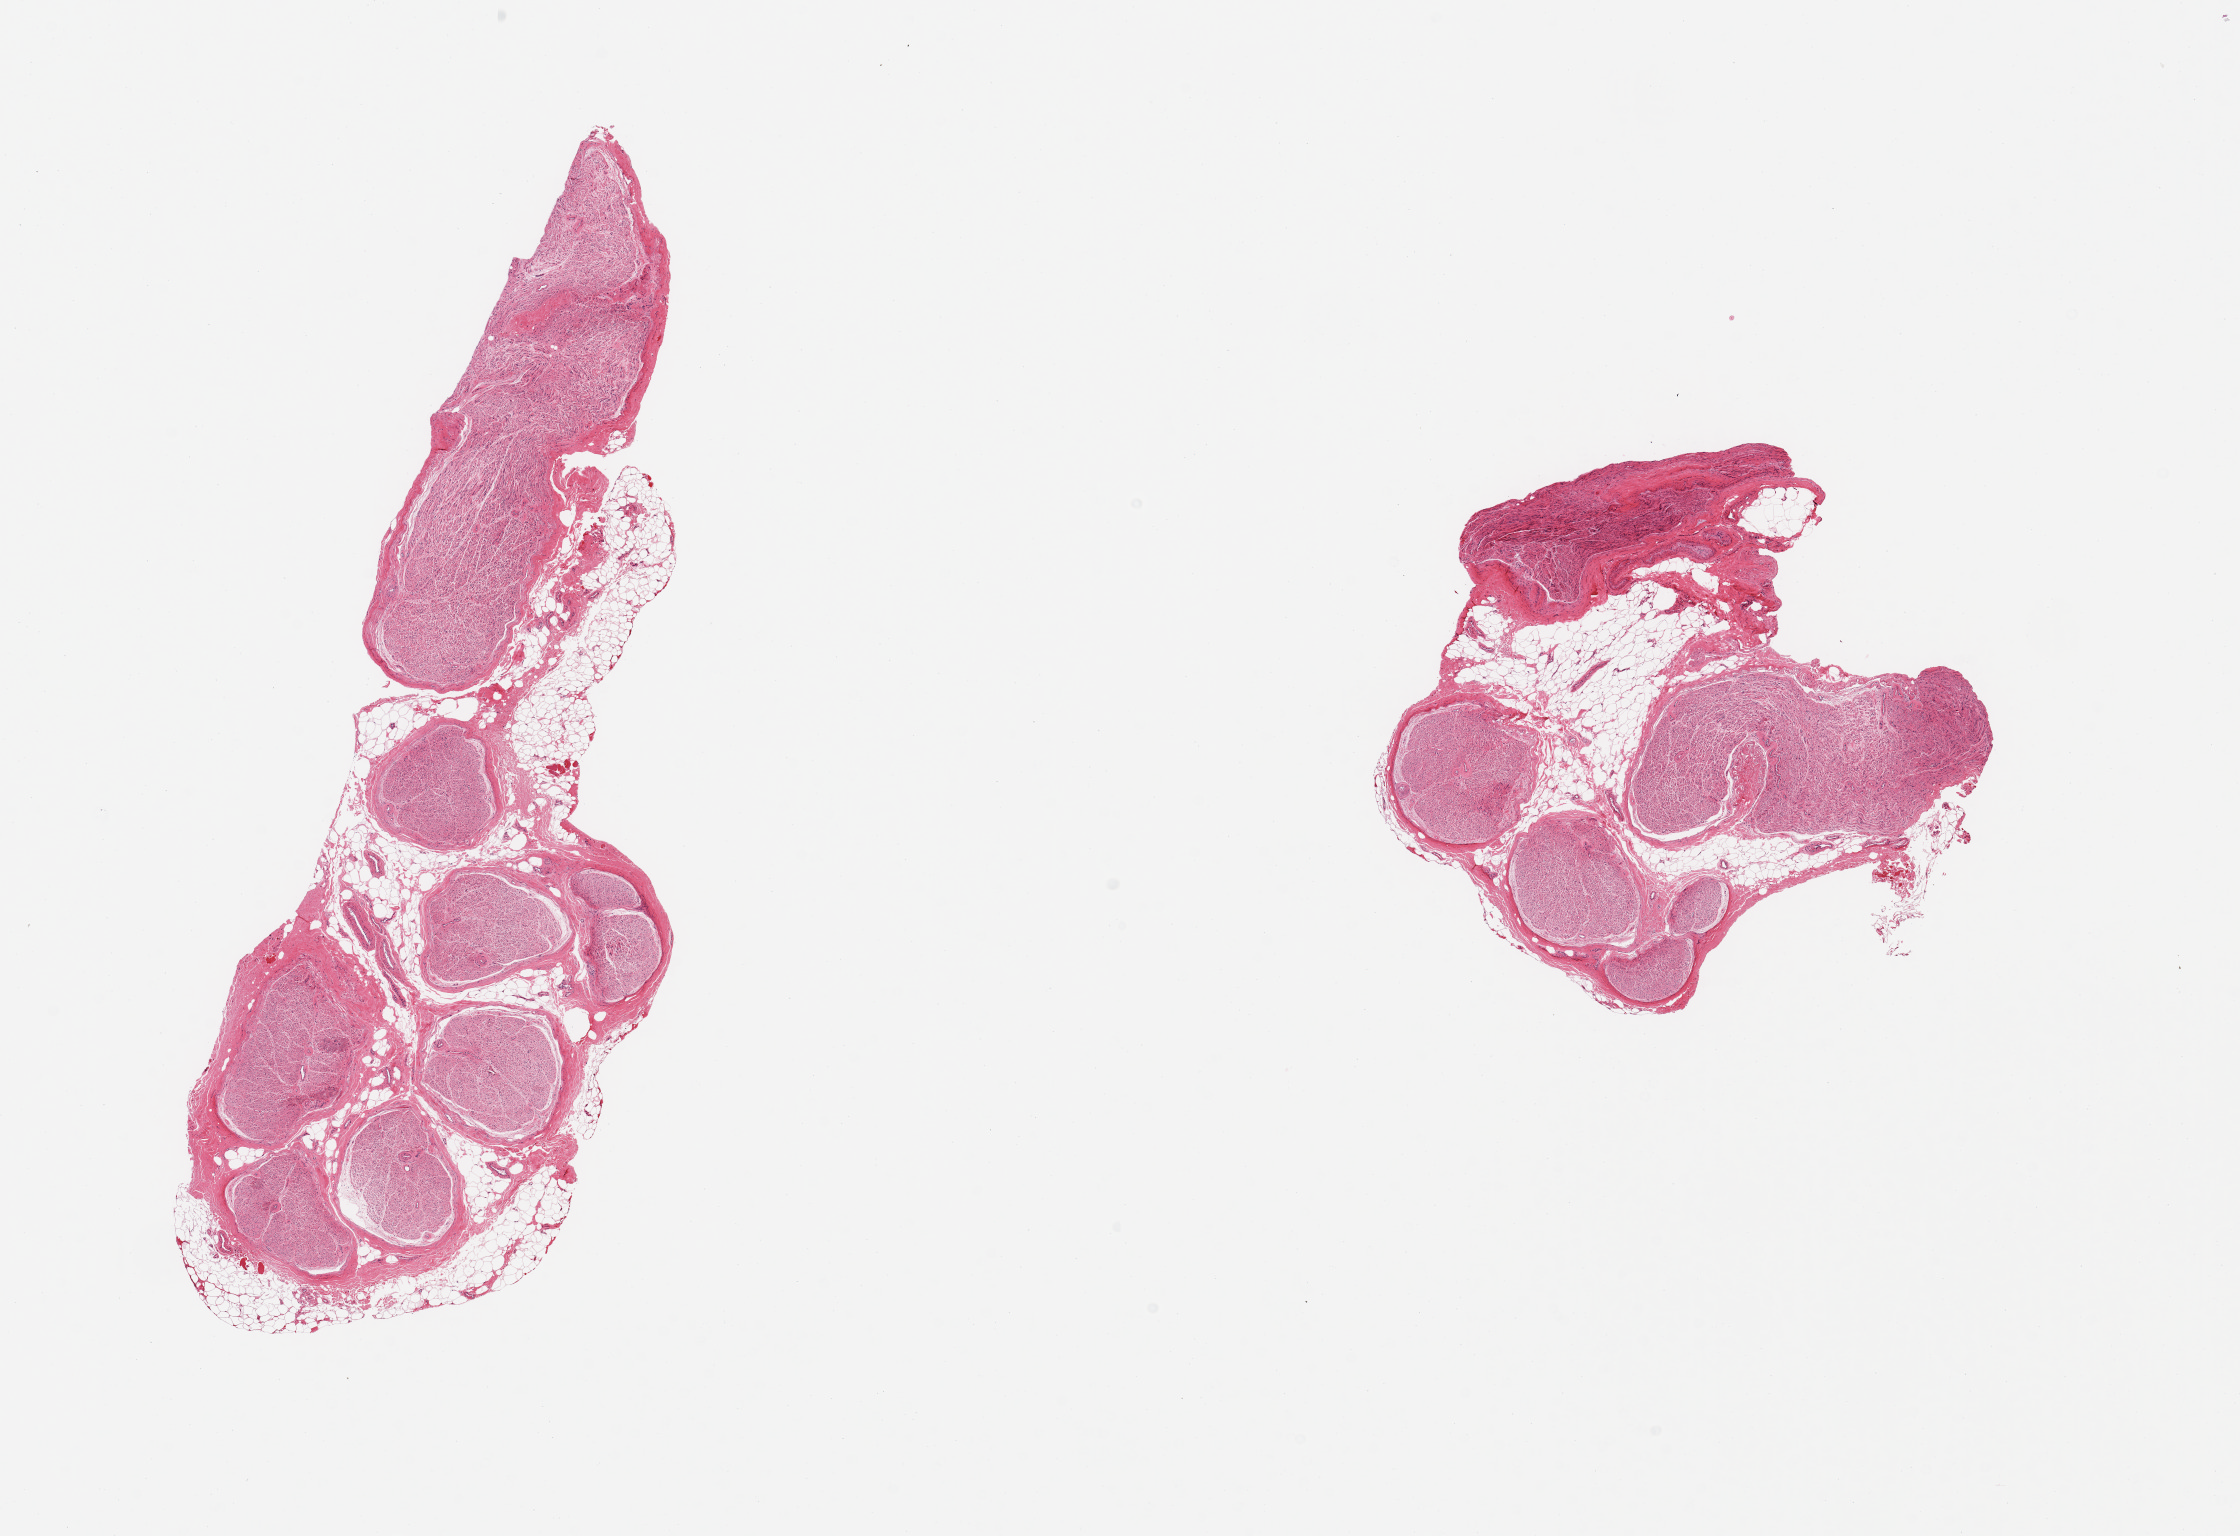
Digitized hematoxylin and eosin (H&E)-stained section — low-resolution overview of the scanned area, about 17.7 x 12.2 mm. PAXgene-fixed, paraffin-embedded tissue. Sampled site (target tissue): tibial nerve. Donor tissue sample. Donor sex: male.
* reviewer comment on this tissue sample: 2 pieces; nerve with 20-30% attached and internal fat